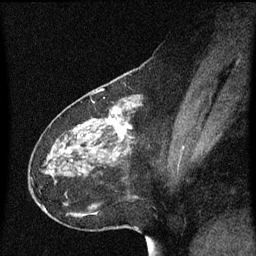
Breast MRI (dynamic contrast-enhanced), one sagittal slice. Position 24 of 60 along the scan axis. Dynamic contrast-enhanced series, image 2 of 3 at this slice position (ordered by acquisition). 1.5 T. TE 4.2 ms, TR 8.4 ms. 2 mm slice thickness. 256 × 256 image matrix, field of view 200 × 200 mm. Female patient, age 49 years. Case-level facts recorded for this patient, not image findings: setting: breast cancer imaged before/during neoadjuvant chemotherapy; receptor status: HR-positive, HER2-negative.
Annotated regions visible in this slice (semi-automatically segmented with operator editing):
- analysis volume of interest (the breast-tissue region the enhancement analysis was run in; not a lesion): box from (x=30, y=96) to (x=144, y=221) px
- tumour enhancement mask (voxels above the 70 % enhancement threshold inside the analysis volume of interest): (x=107, y=110)–(x=129, y=135)